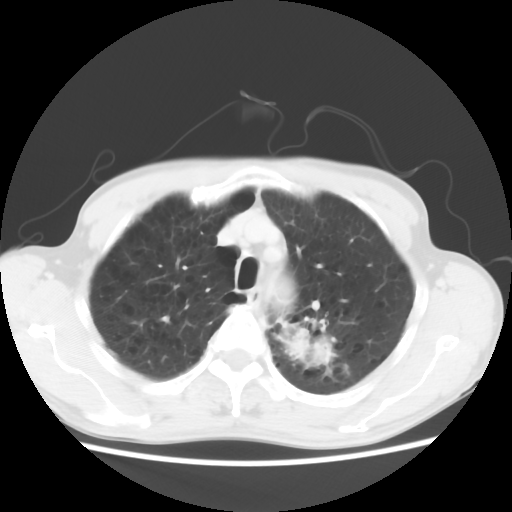
Chest CT, one axial slice. Slice 50 of 64 in the series (ordered by position). 120 kVp. Lung window (W 1500 / L -600 HU). 5 mm slice thickness. 512 × 512 image matrix. Male patient, age 63 years. Case-level facts recorded for this patient, not image findings: clinical TNM (as recorded): T2 N0 M0.
Structures marked on this image (bounding box drawn by a radiologist):
- lung tumour (recorded histology: adenocarcinoma): bounding box [x1, y1, x2, y2] px = [277, 317, 336, 375]